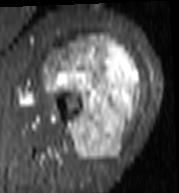
MRI of an extremity soft-tissue mass, one axial slice. Slice 63 of 103 in the series (ordered by position). STIR. MR volume resampled by the dataset authors to the PET/CT grid (not the native acquisition matrix). 3.27 mm slice thickness. 179 × 193 image matrix, field of view 175 × 188 mm. Female patient. From the clinical record (not read from this slice): histological type: undifferentiated – high grade; grade: high; site of the primary tumour: left thigh.
Structures marked on this image (expert contour drawn on MRI and transferred to this co-registered scan by the dataset authors):
- gross tumour volume including surrounding oedema: bounding box (x1, y1, x2, y2) in pixels: (43, 35, 142, 161)
- gross tumour volume (mass): (43, 35, 140, 161)